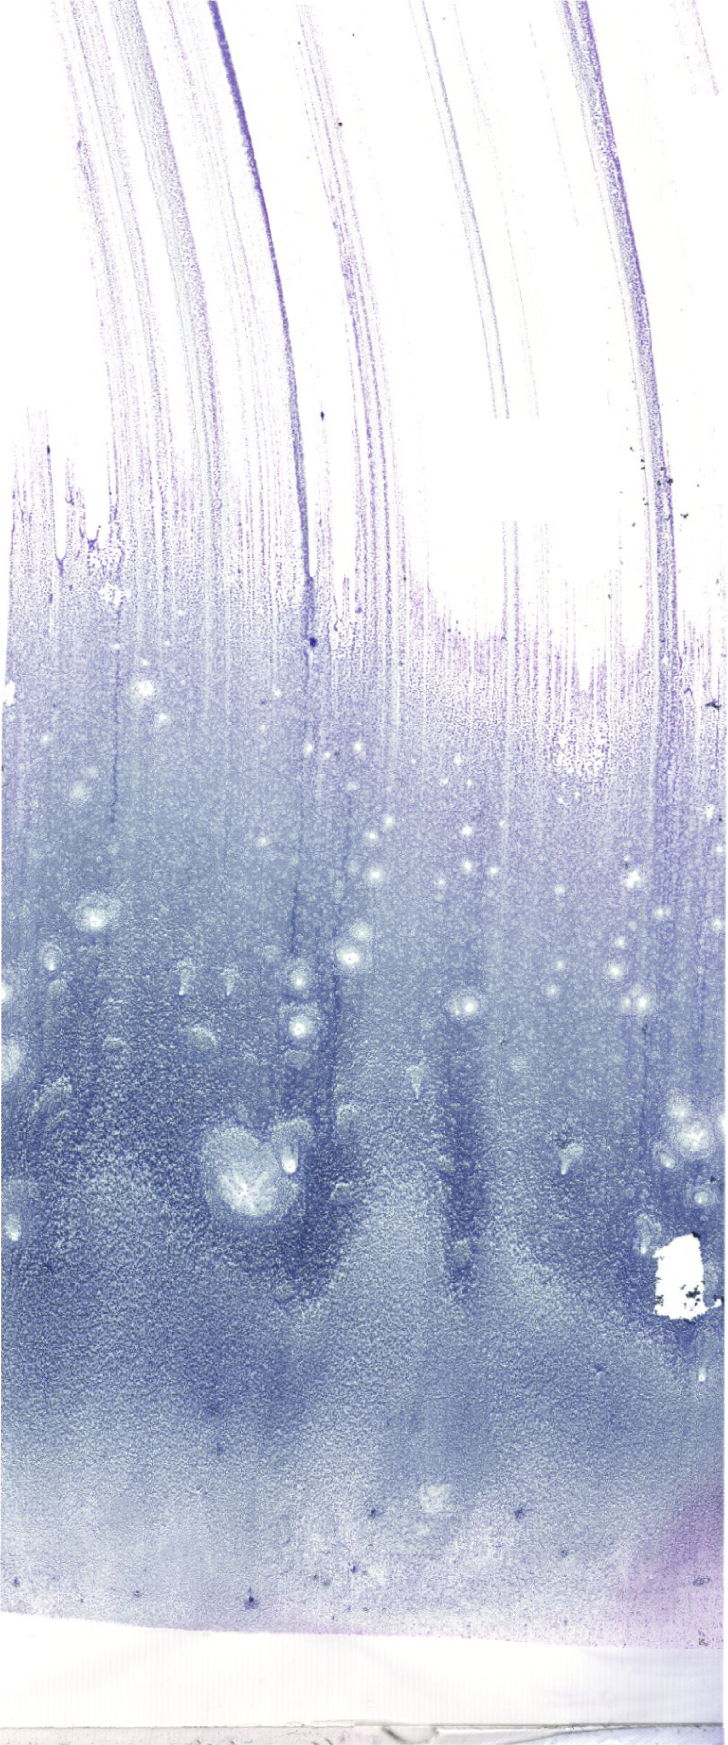
Whole-slide image of a May-Grünwald–Giemsa-stained bone marrow aspirate smear — low-resolution overview of the scanned area, about 20.6 x 49.5 mm. Patient sex: male.
* diagnosis: B Acute Lymphoblastic Leukemia